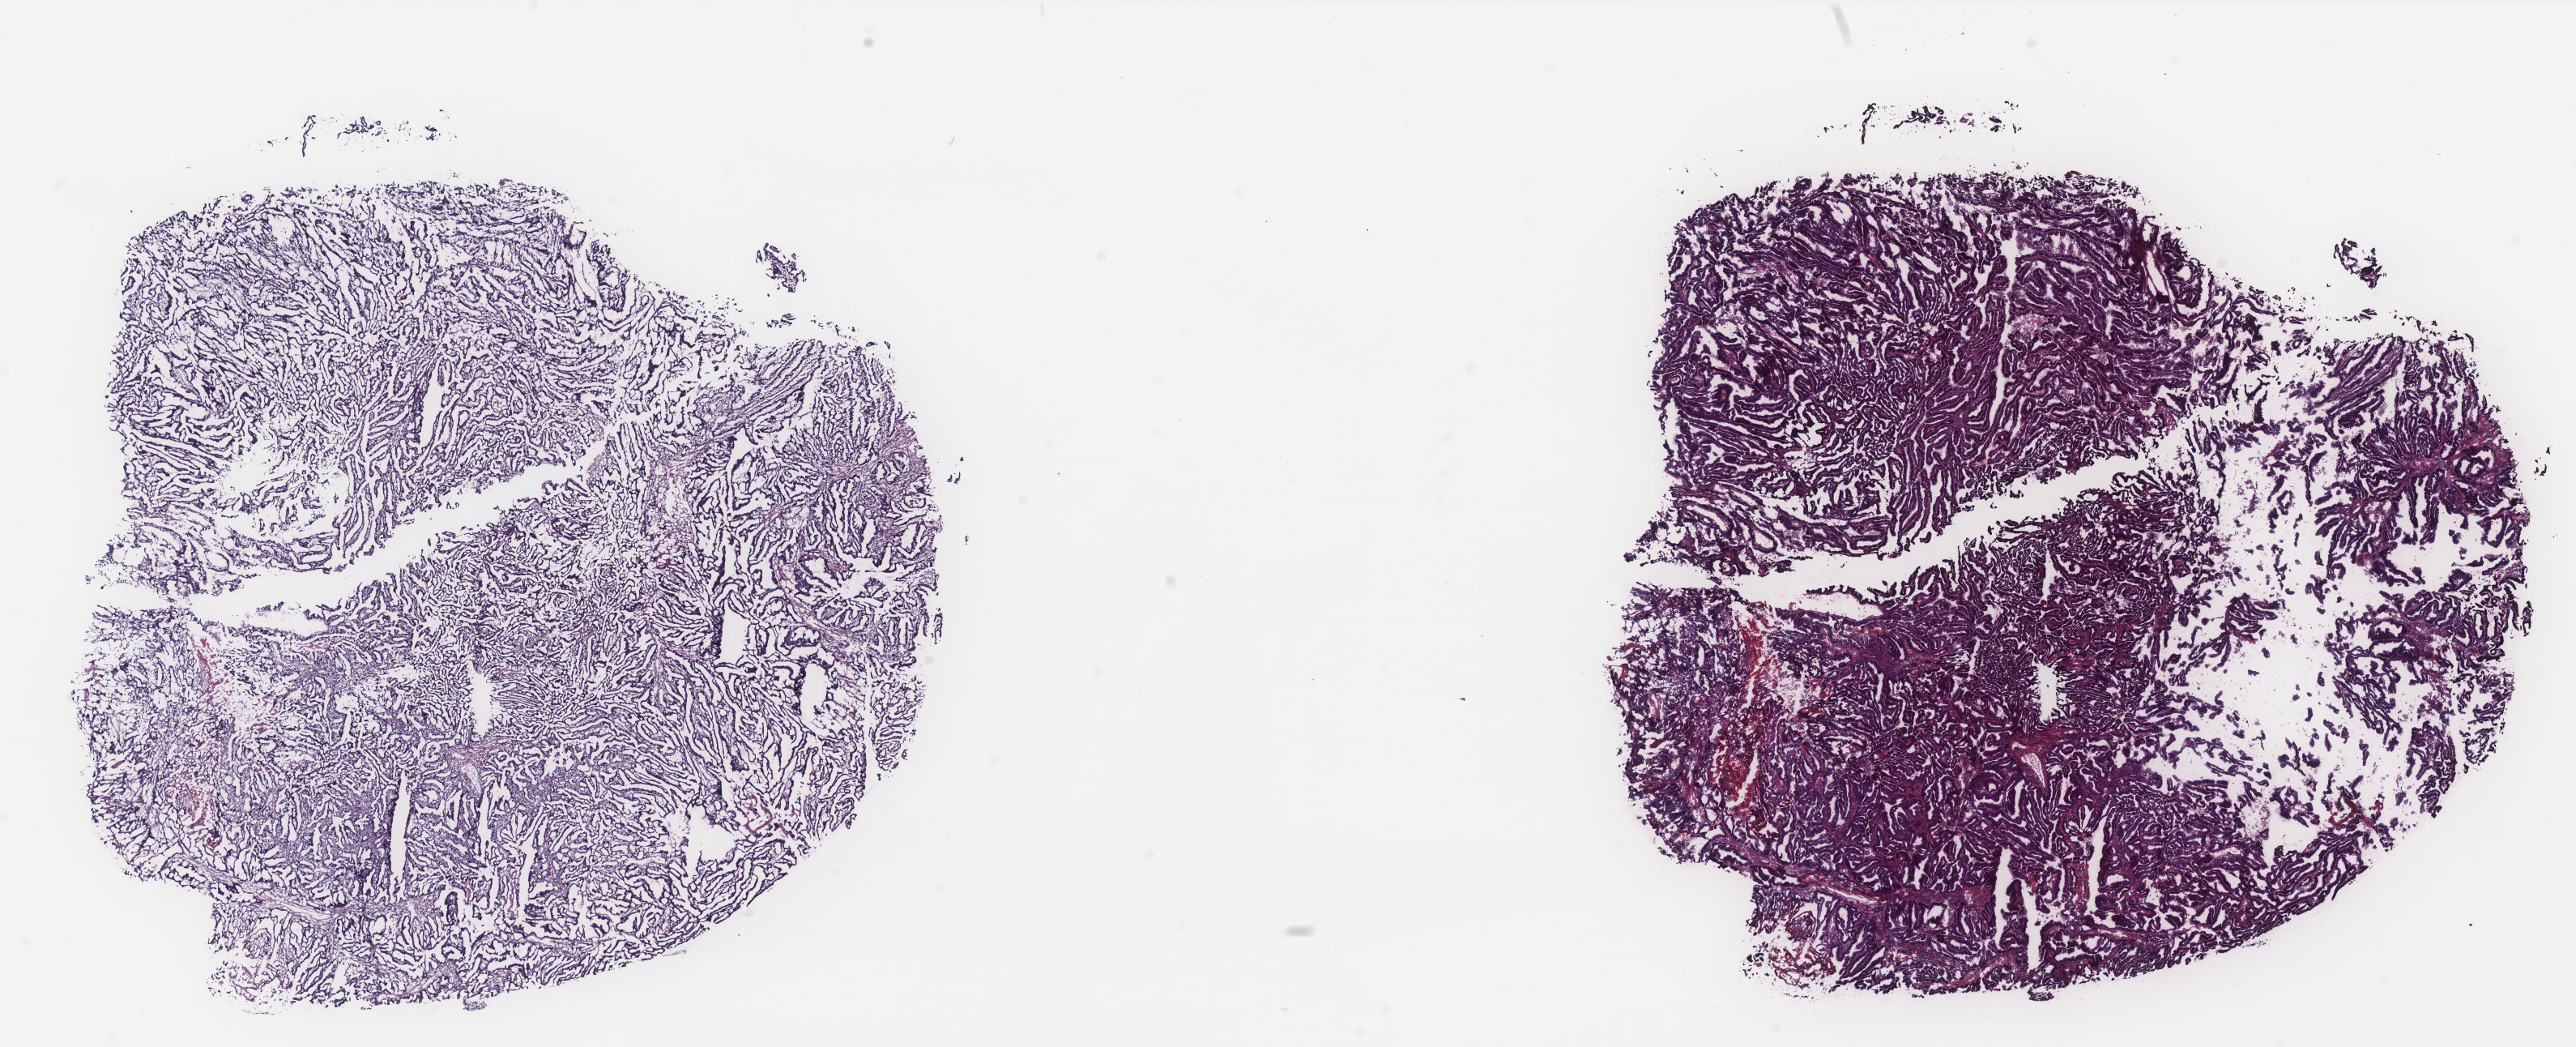
Whole-slide histology image, H&E — a low-resolution overview of the entire scanned area, about 25.5 x 10.4 mm (from a 40x scan), frozen section, sample: primary tumour, uterus. Female patient; age at initial diagnosis 55 years. Histologic grade: G1 (well differentiated). Composition of this section per pathologist review: tumour cells 80%, tumour nuclei 80%, normal cells 0%, stromal cells 20%, necrosis 0%. Infiltration values recorded for this section: lymphocyte infiltration 40%, monocyte infiltration 10%, neutrophil infiltration 30%.
Pathologic diagnosis: Endometrioid adenocarcinoma, NOS (endometrium). FIGO stage: IIIC. Lymph nodes positive (case pathology): 3 of 4 examined.